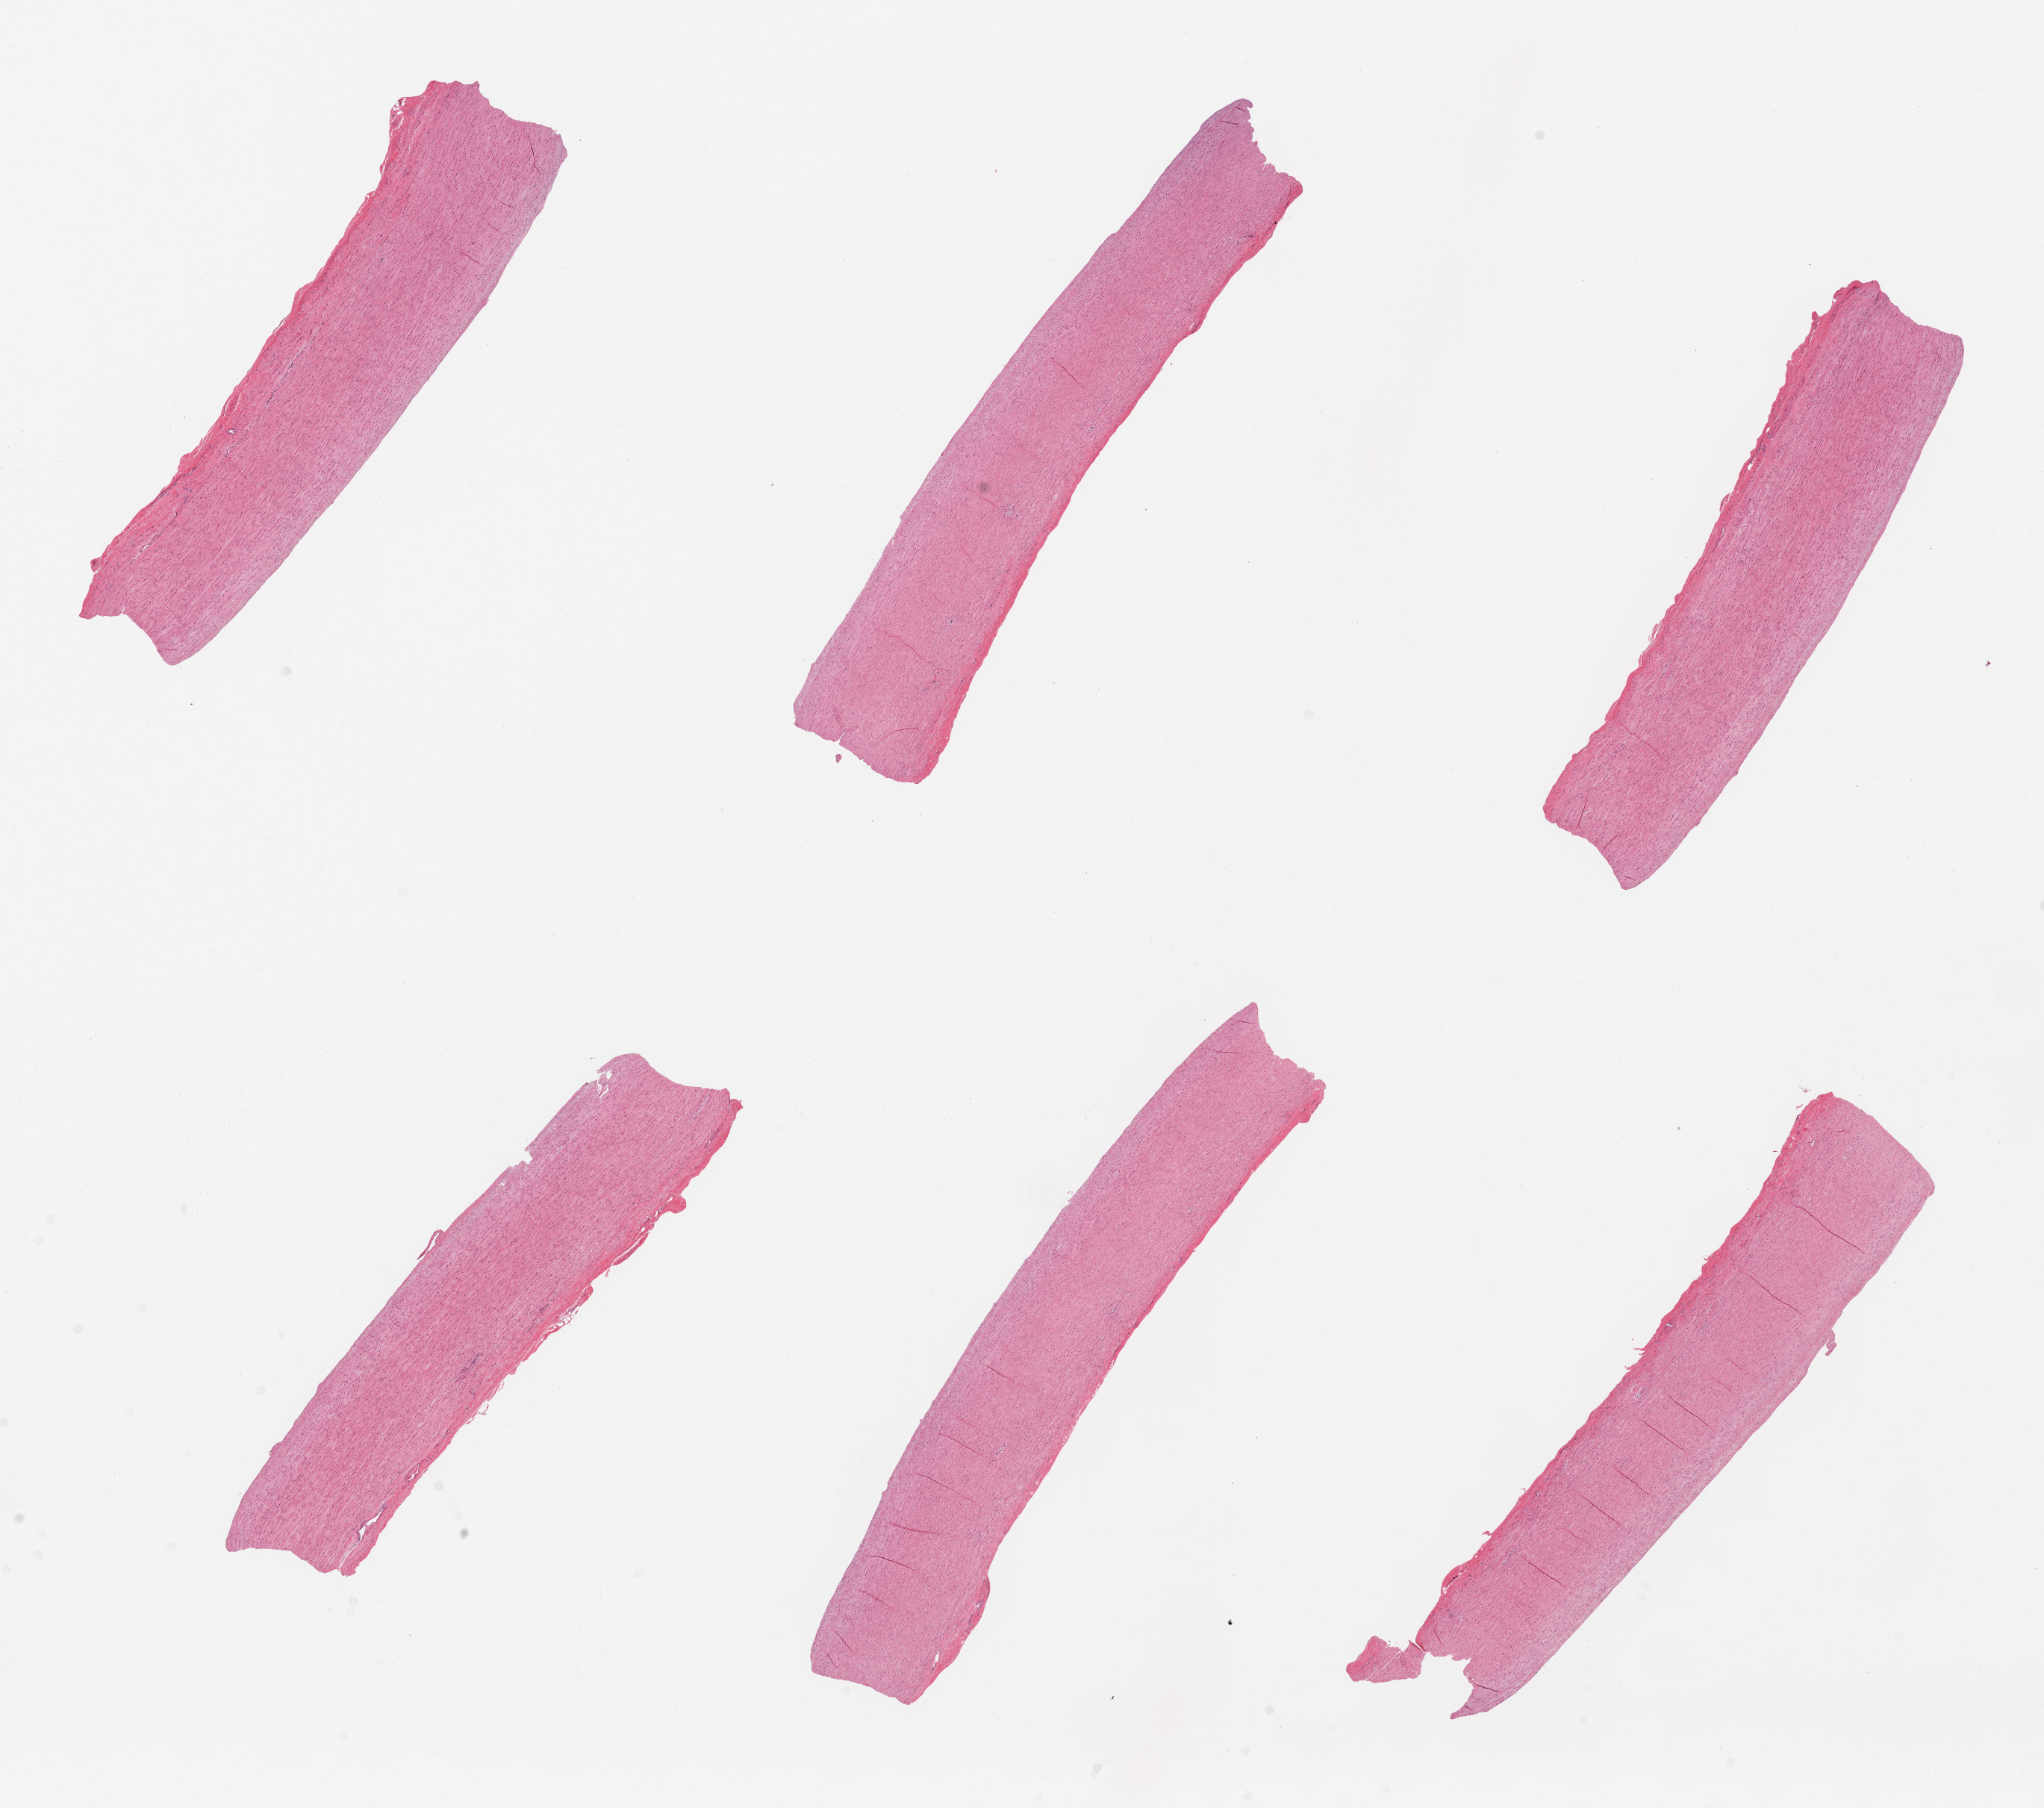
H&E whole-slide image, whole scanned area (about 21.7 x 19.2 mm, acquisition: 20x scan) shown as a low-resolution overview; PAXgene-fixed paraffin-embedded (PFPE) section; section of aorta (target tissue); donor tissue sample. Donor: male.
Pathologist's review note for this sample: 6 pieces; no pathologic changes.